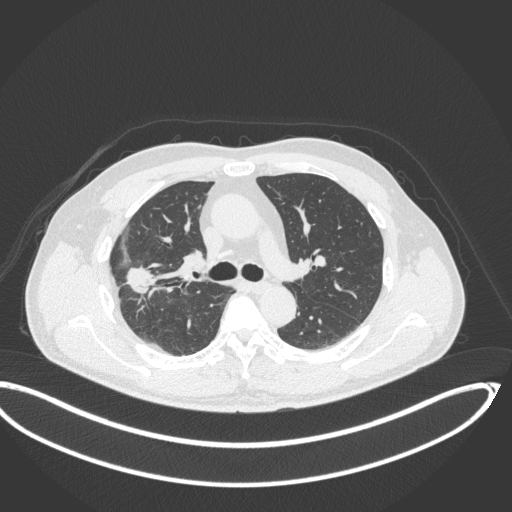
Chest CT, one axial slice; slice 221 of 341 in the series (ordered by position); 120 kVp; lung window (W 1500 / L -600 HU); 1 mm slice thickness; 512 × 512 image matrix, field of view 439 × 439 mm. Patient: male, 63 years. Case-level facts recorded for this patient, not image findings: clinical TNM (as recorded): T1c N0 M0.
Outlined on this slice (bounding box drawn by a radiologist):
- lung tumour (recorded histology: adenocarcinoma): bounding box <122,262,161,304> (left, top, right, bottom; pixels)